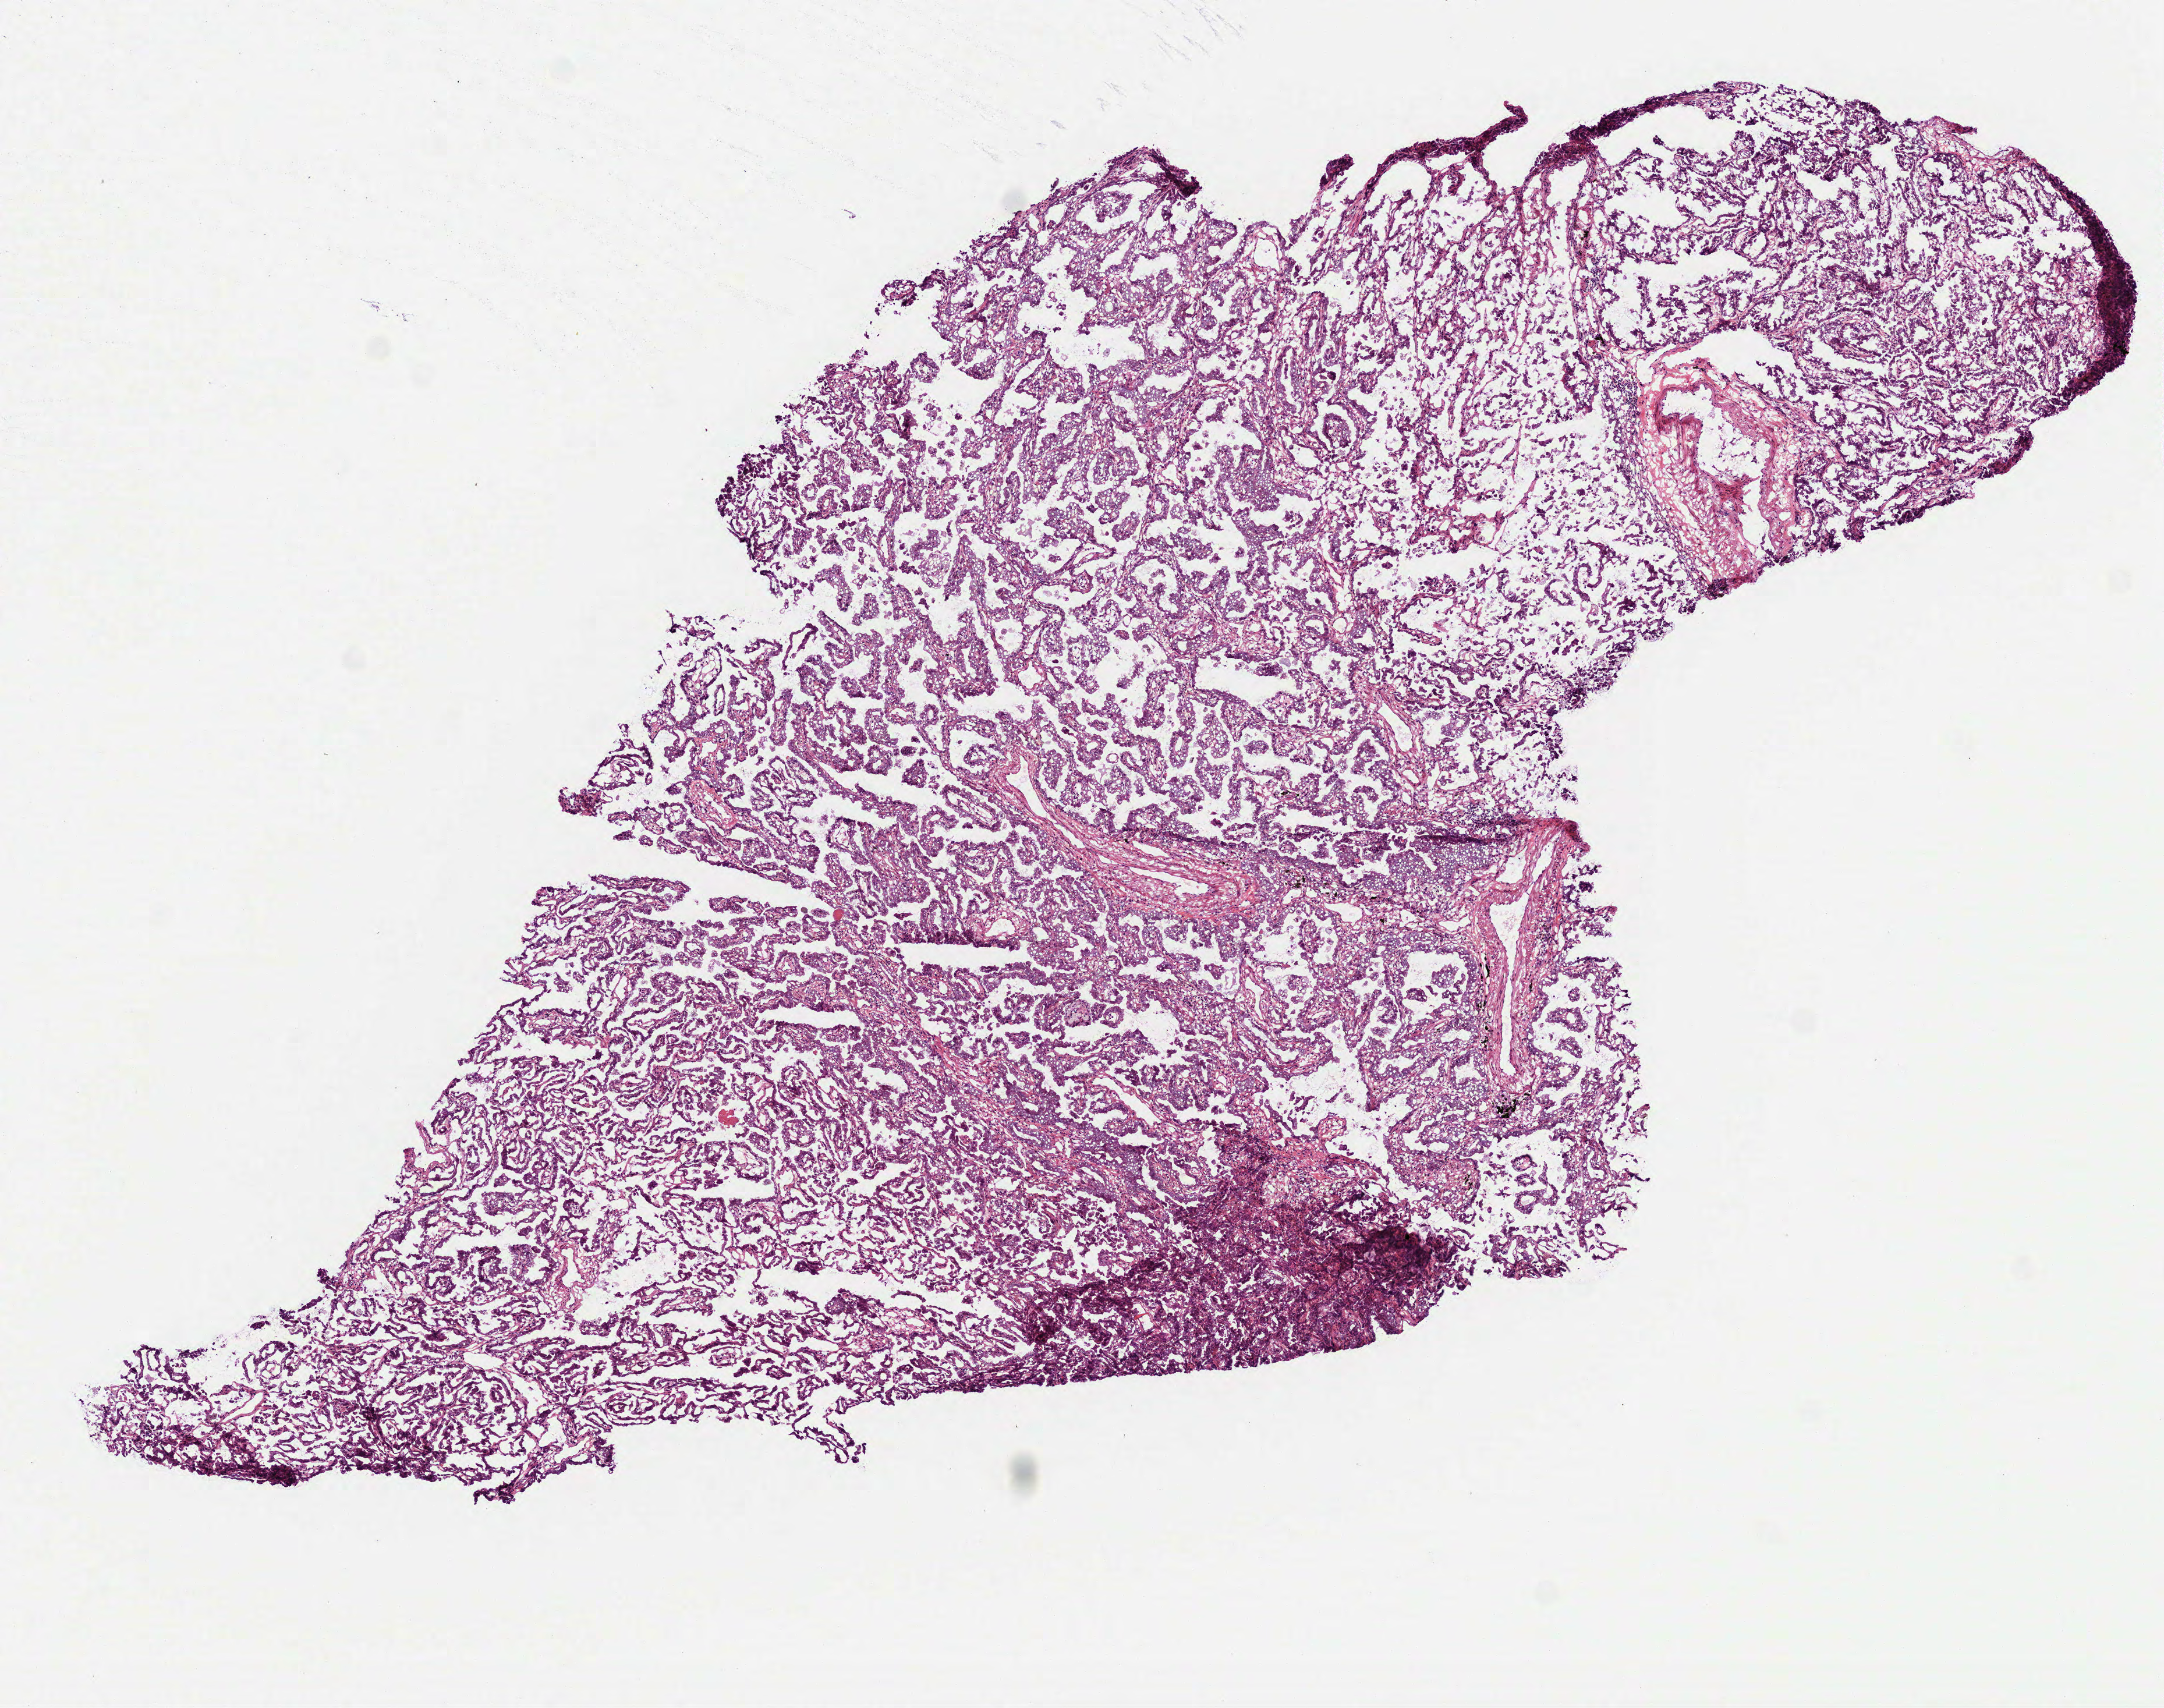
H&E-stained whole-slide image — low-resolution overview of the scanned area, about 7.5 x 5.9 mm, frozen section from the top of the tissue portion, primary tumour sample from the lung. Patient: male, age at initial diagnosis 71 years. Slide review estimates, as recorded: tumour cells 80%, tumour nuclei 75%, normal cells 0%, stromal cells 15%, necrosis 5%.
Pathologic diagnosis: Adenocarcinoma with mixed subtypes (lower lobe, lung). Laterality: right. AJCC pathologic stage: IIIB (6th edition).